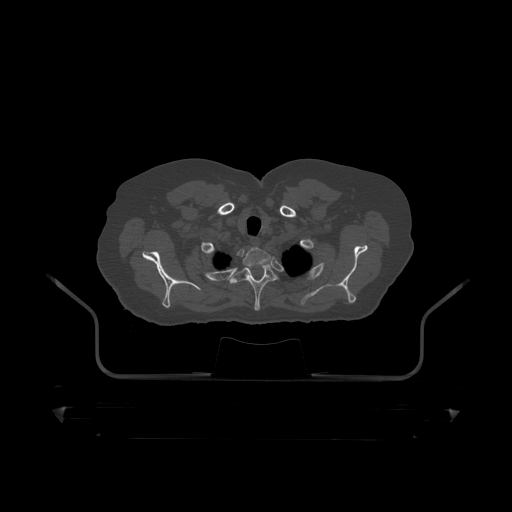
CT including the spine, one axial slice; position 379 of 390 along the scan axis; reconstruction kernel STANDARD; 120 kVp; bone window (W 1800 / L 400 HU); 512 × 512 image matrix. Male patient, age 60 years. Case-level facts recorded for this patient, not image findings: primary cancer: prostate.
Annotated regions visible in this slice (semi-automatically segmented with operator editing):
- T1 vertebra: bounding box [x1, y1, x2, y2] px = [212, 245, 271, 267]
- T2 vertebra: [230, 263, 277, 312]